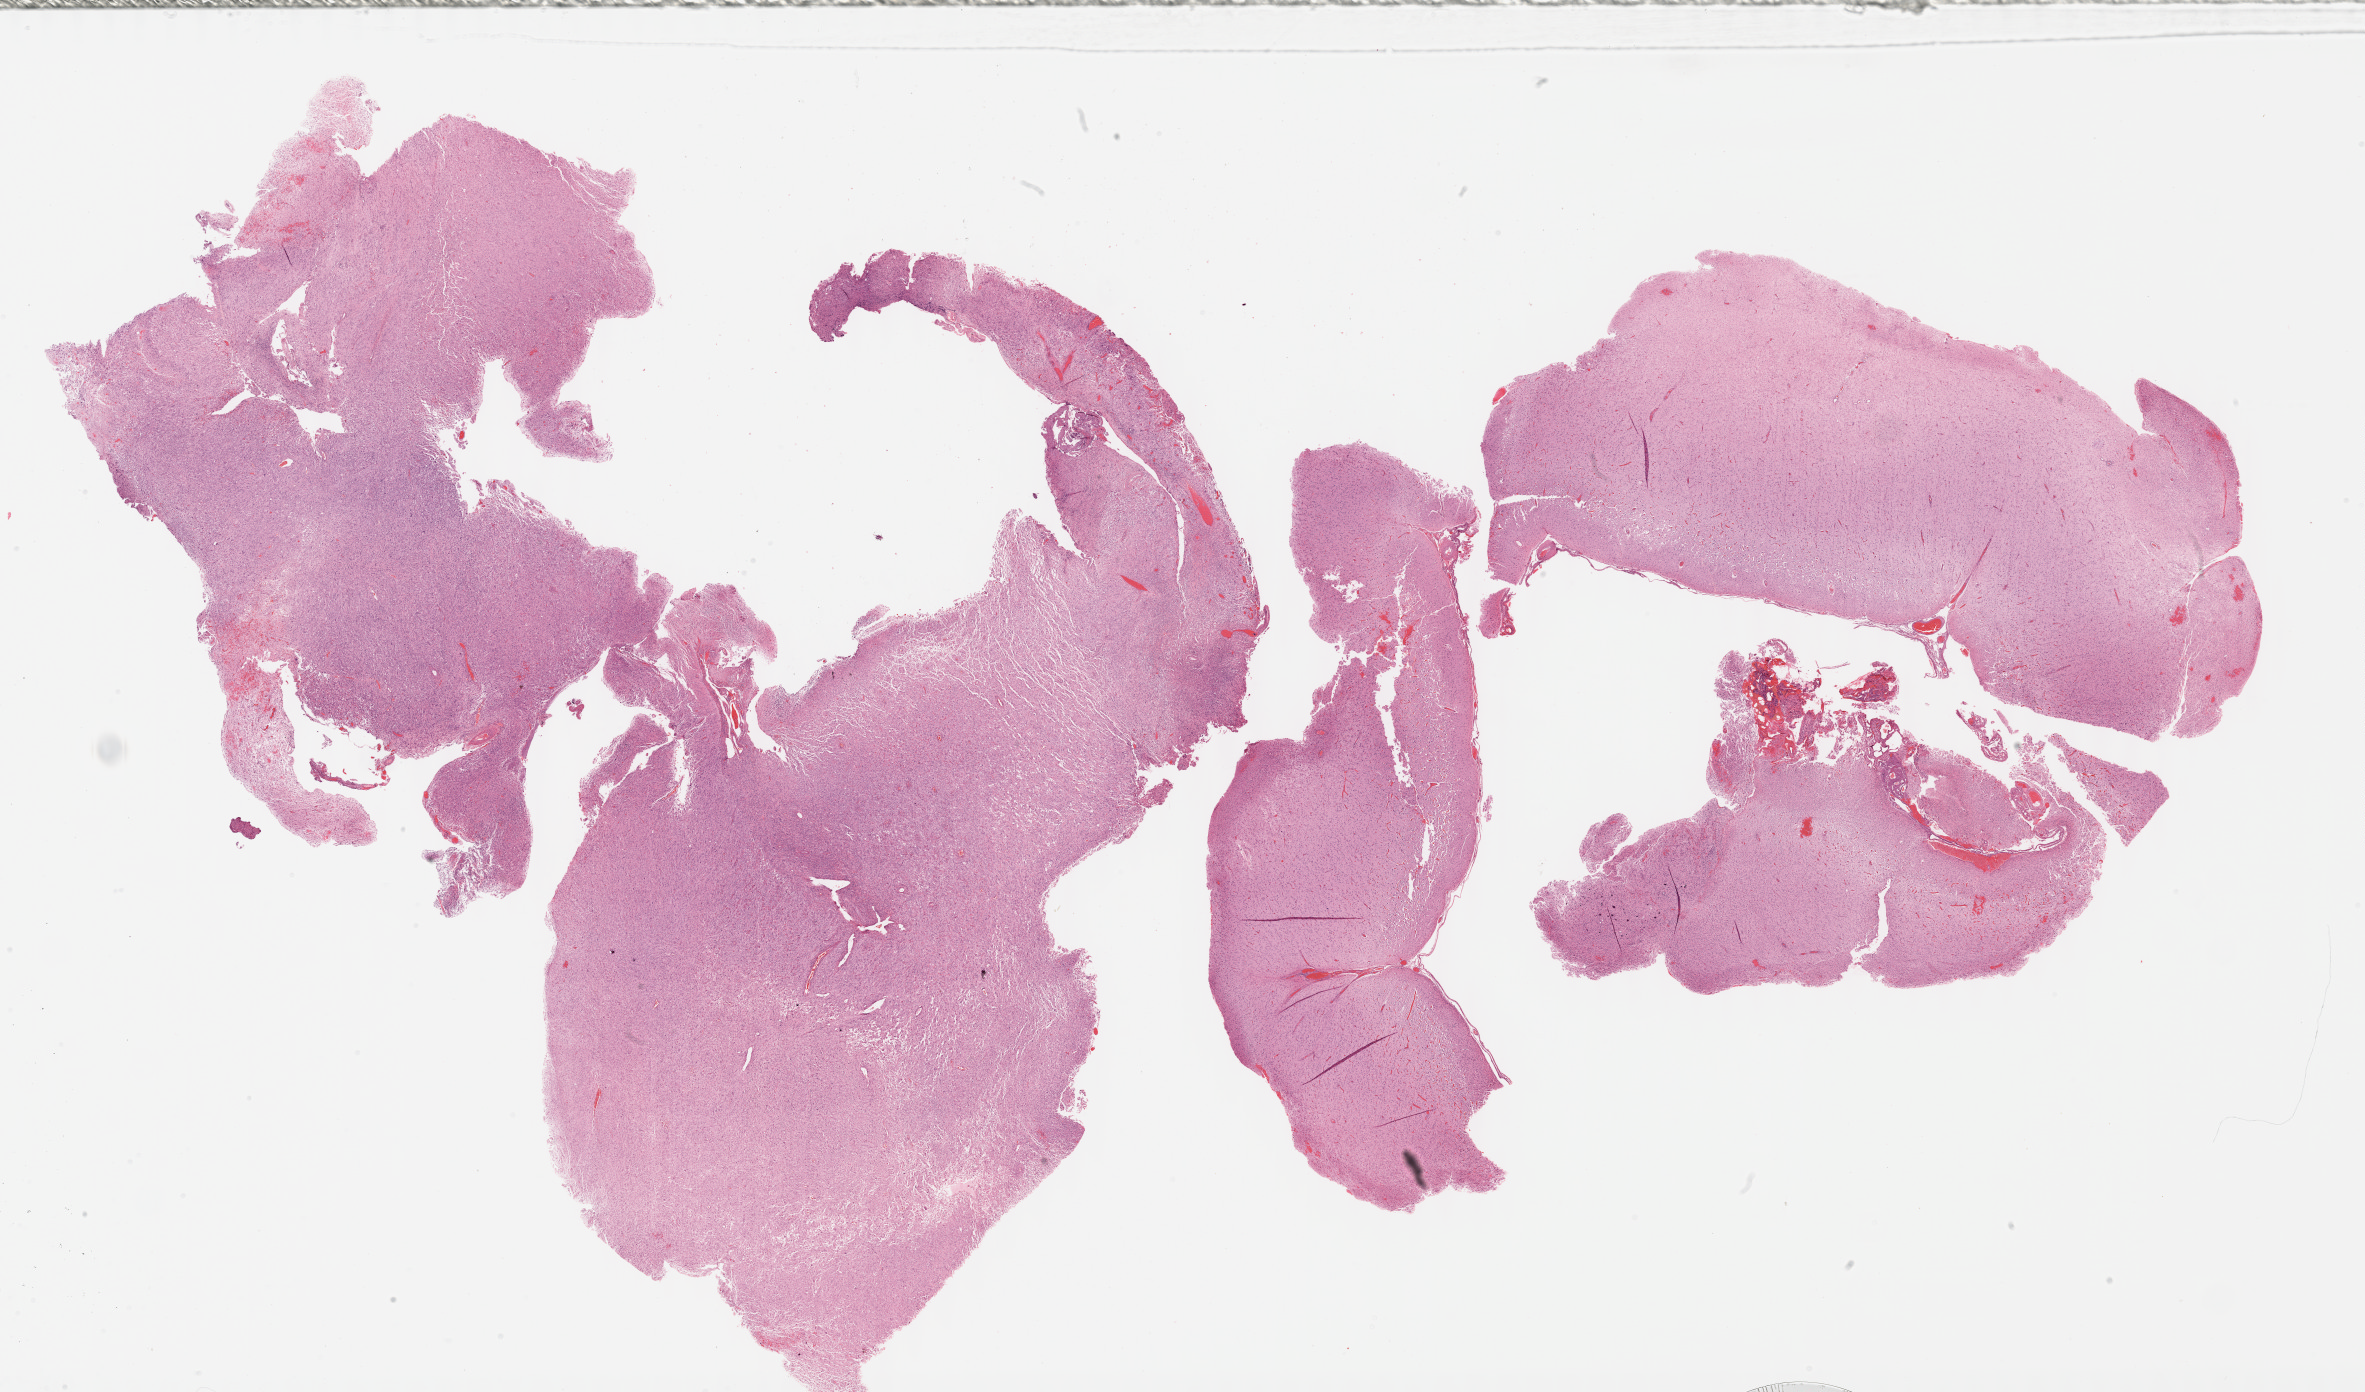
Whole-slide histology image, H&E-stained, whole scanned area (about 38.2 x 22.5 mm) shown as a low-resolution overview. Formalin-fixed paraffin-embedded (FFPE) diagnostic section. Primary tumour sample from the brain. Male, age 14 years at initial diagnosis.
Pathologic diagnosis: Glioblastoma.